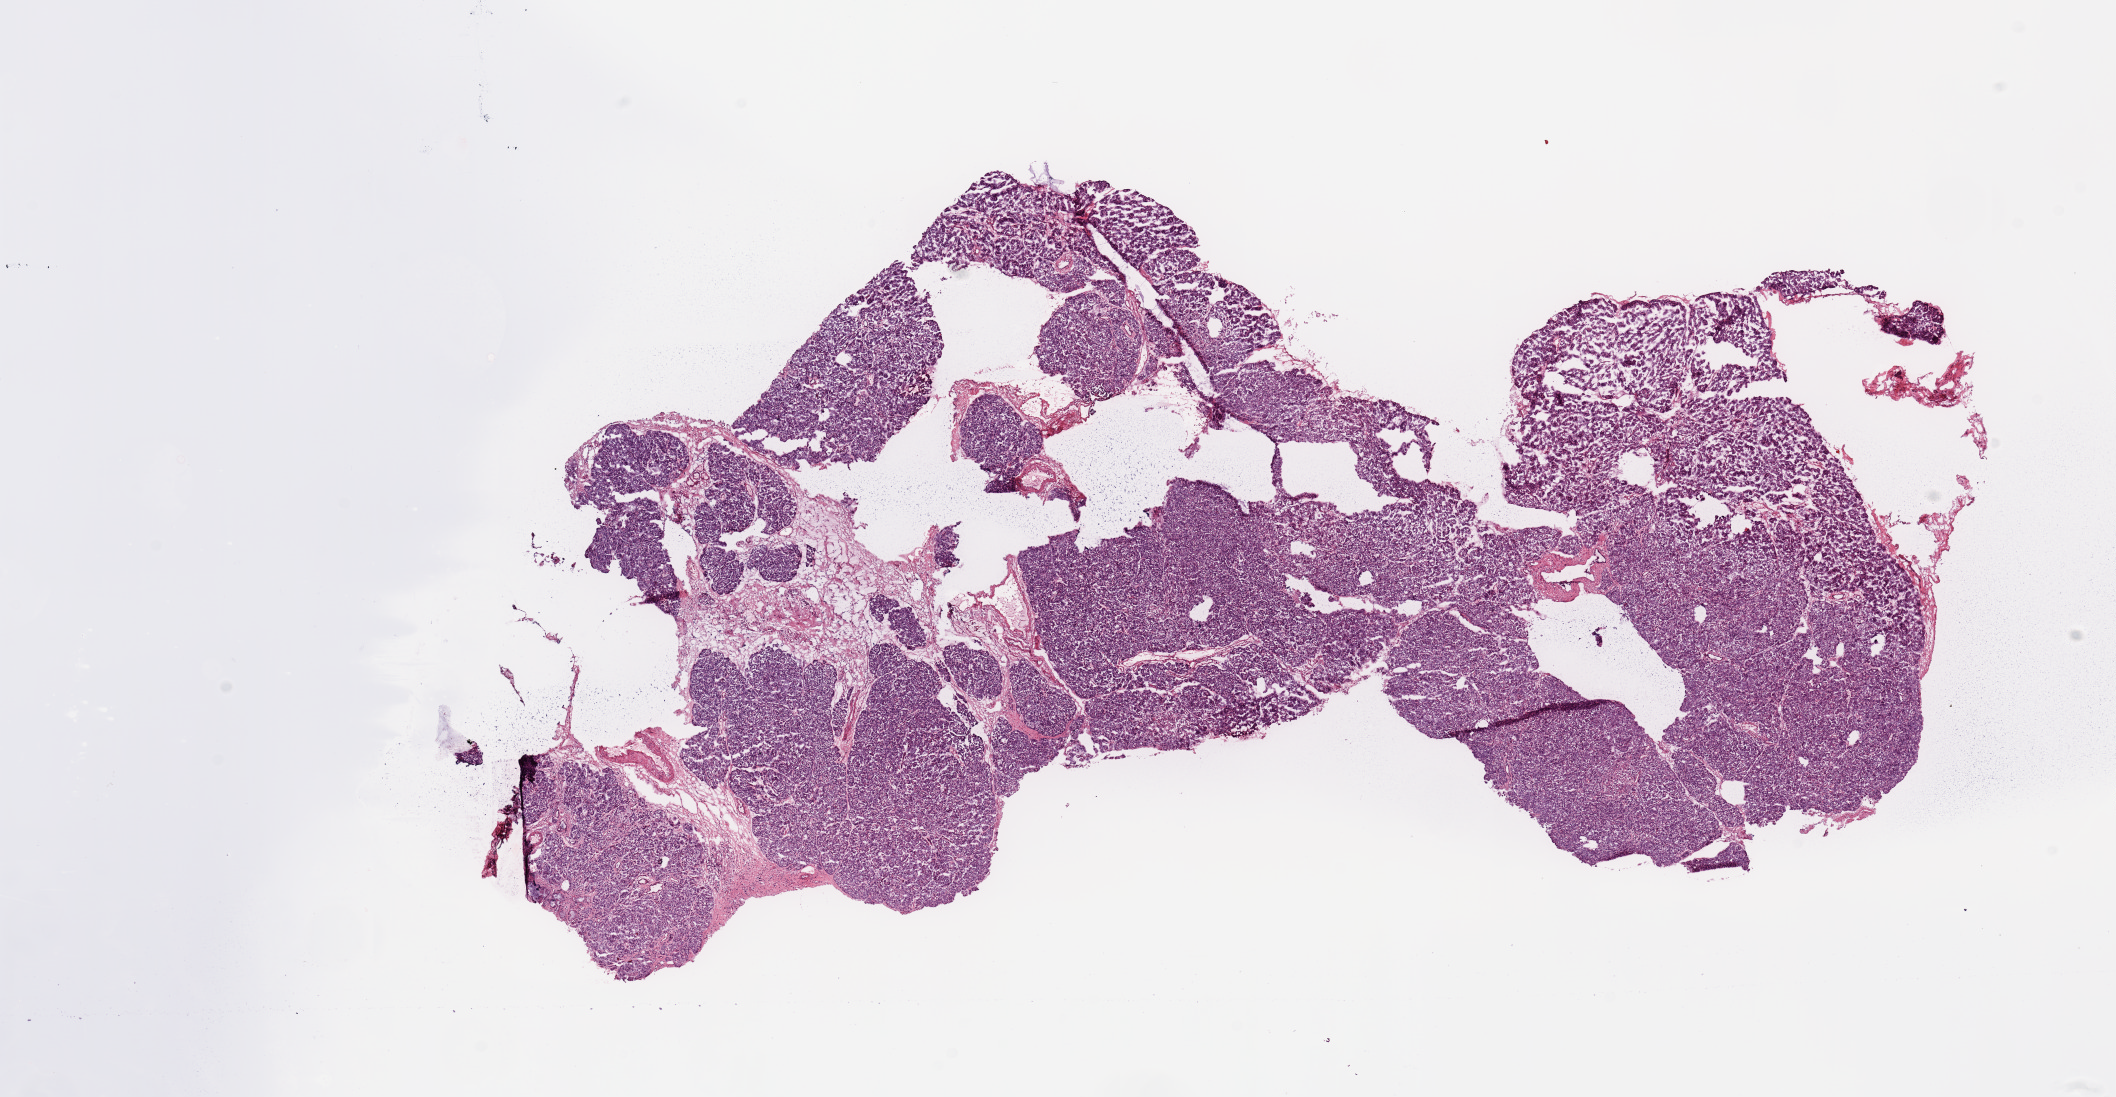
H&E whole-slide image, low-resolution overview of the scanned area, about 16.7 x 8.7 mm (acquisition: 20x scan). Pancreas, normal (non-tumour) tissue. Patient: male, age 69 years.
• this section: normal (non-tumour) tissue from the same patient
• patient diagnosis: Infiltrating duct carcinoma, NOS